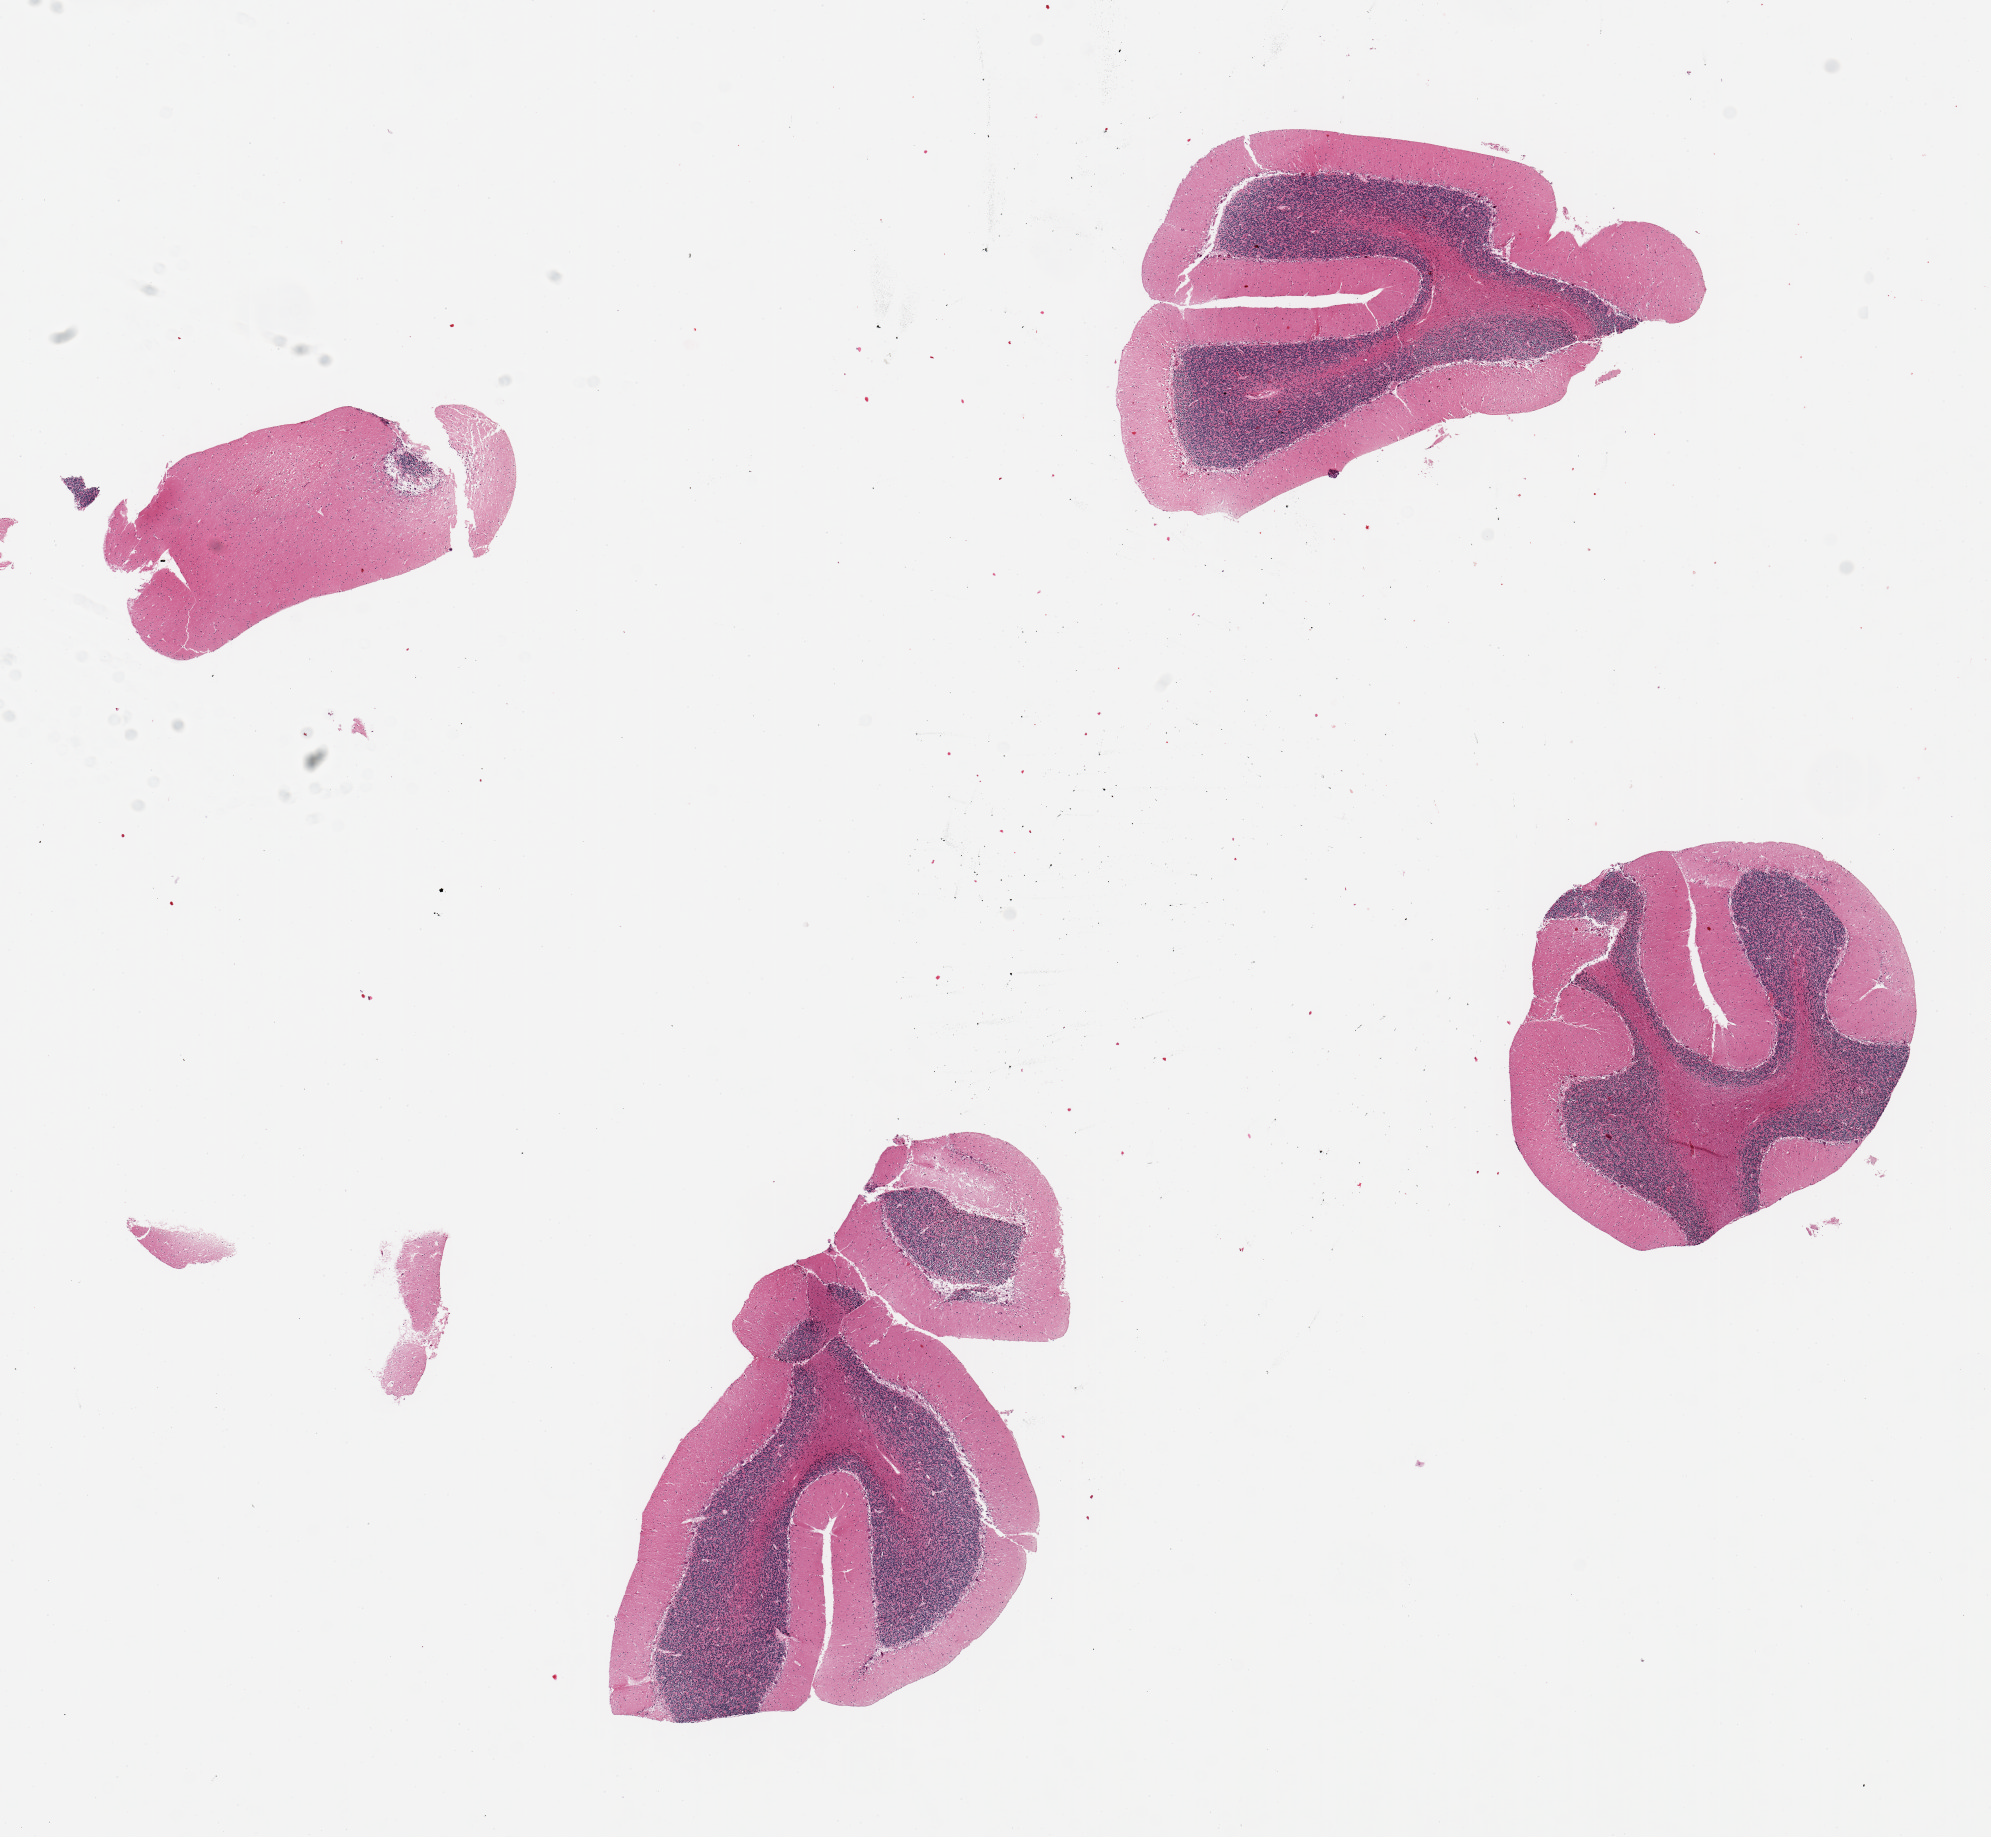
Hematoxylin and eosin (H&E) whole-slide image — shown as a low-resolution overview of the whole scanned area (about 15.8 x 14.5 mm). PAXgene-fixed, paraffin-embedded tissue. Target tissue: cerebellum. Tissue donor sample.
Pathologist's review note for this sample: 4 pieces, up to 5x3mm; ischemic changes in Purkinje cells.